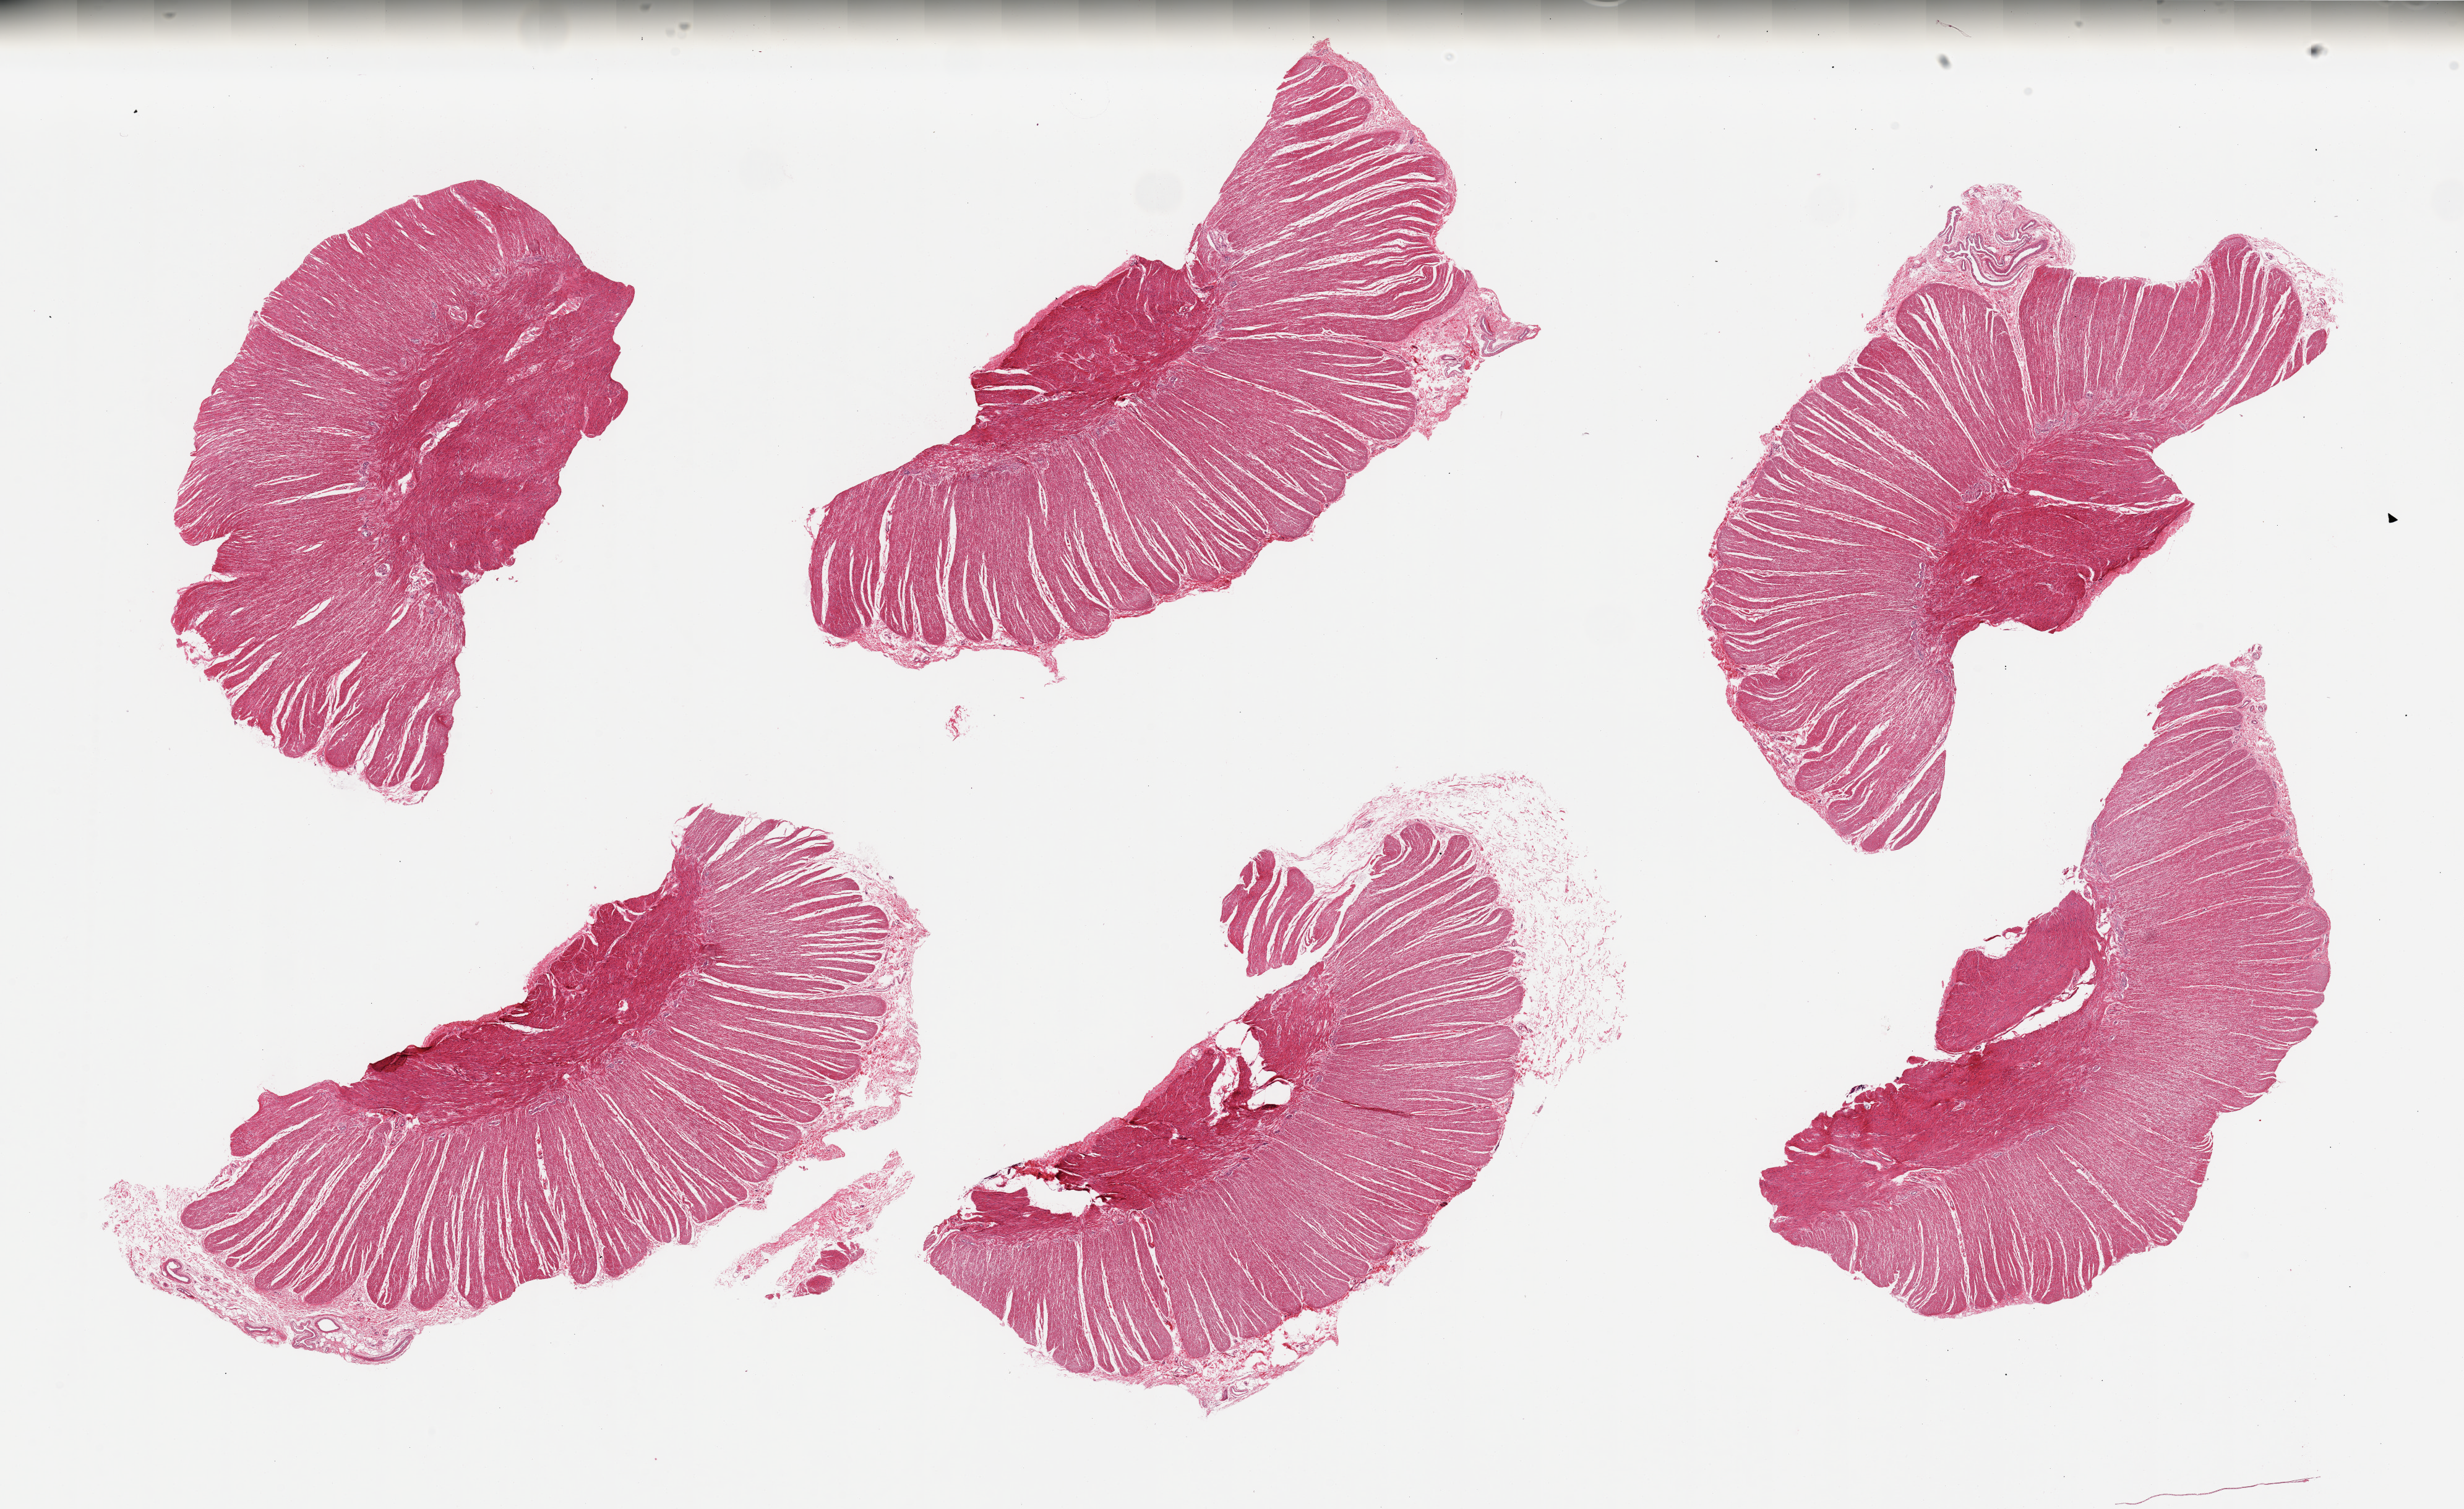
Digitized H&E-stained section, whole scanned area (about 31.5 x 19.3 mm, acquisition: 20x scan) shown as a low-resolution overview. PAXgene-fixed, paraffin-embedded tissue. Sampled site (target tissue): sigmoid colon. Tissue donor sample. Donor sex: male.
Reviewer comment on this tissue sample: 6 pieces. Well trimmed thick muscularis.